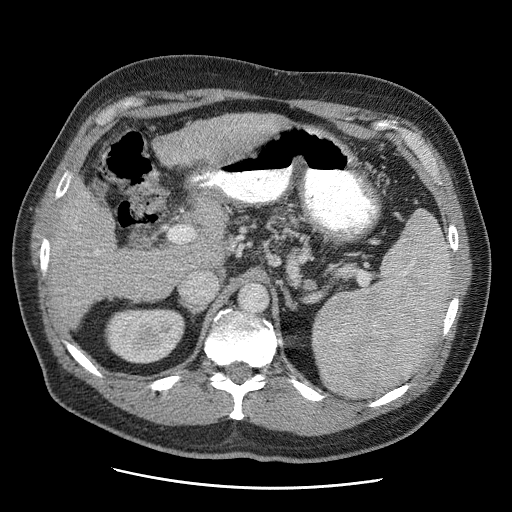
Contrast-enhanced abdominal CT (liver protocol), one axial slice. Position 25 of 81 along the scan axis. Reconstruction kernel STANDARD. 120 kVp. Soft-tissue window (W 400 / L 40 HU). 2.5 mm slice thickness. 512 × 512 image matrix. From the clinical record (not read from this slice): diagnosis: hepatocellular carcinoma (patient treated with transarterial chemoembolisation; whether this scan precedes or follows treatment is not stated here); TNM stage (as recorded): Stage-IIIA; Child-Pugh class: A; tumour differentiation: moderately differentiated; tumour nodularity: multinodular.
Annotated regions visible in this slice (semi-automatic segmentation, software-assisted and operator-edited):
- abdominal aorta: box from (x=240, y=285) to (x=268, y=313) px
- liver parenchyma outside the tumour (the mass and vessels are separate outlines, so this box may not span the whole liver): (x=51, y=114)–(x=288, y=326)